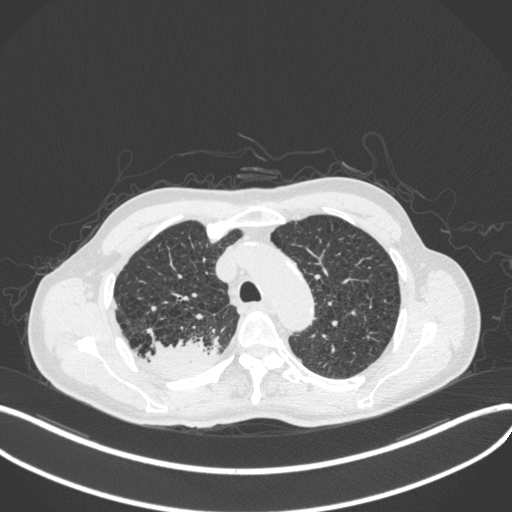
Chest CT, one axial slice. 120 kVp. Lung window (W 1500 / L -600 HU). 1 mm slice thickness. 512 × 512 image matrix. Patient: male, 79 years. Case-level facts recorded for this patient, not image findings: clinical TNM (as recorded): T3 N0 M0.
Structures marked on this image (rectangle marked by the reading radiologist):
- lung tumour (recorded histology: adenocarcinoma): bounding box [x1, y1, x2, y2] px = [140, 332, 224, 376]